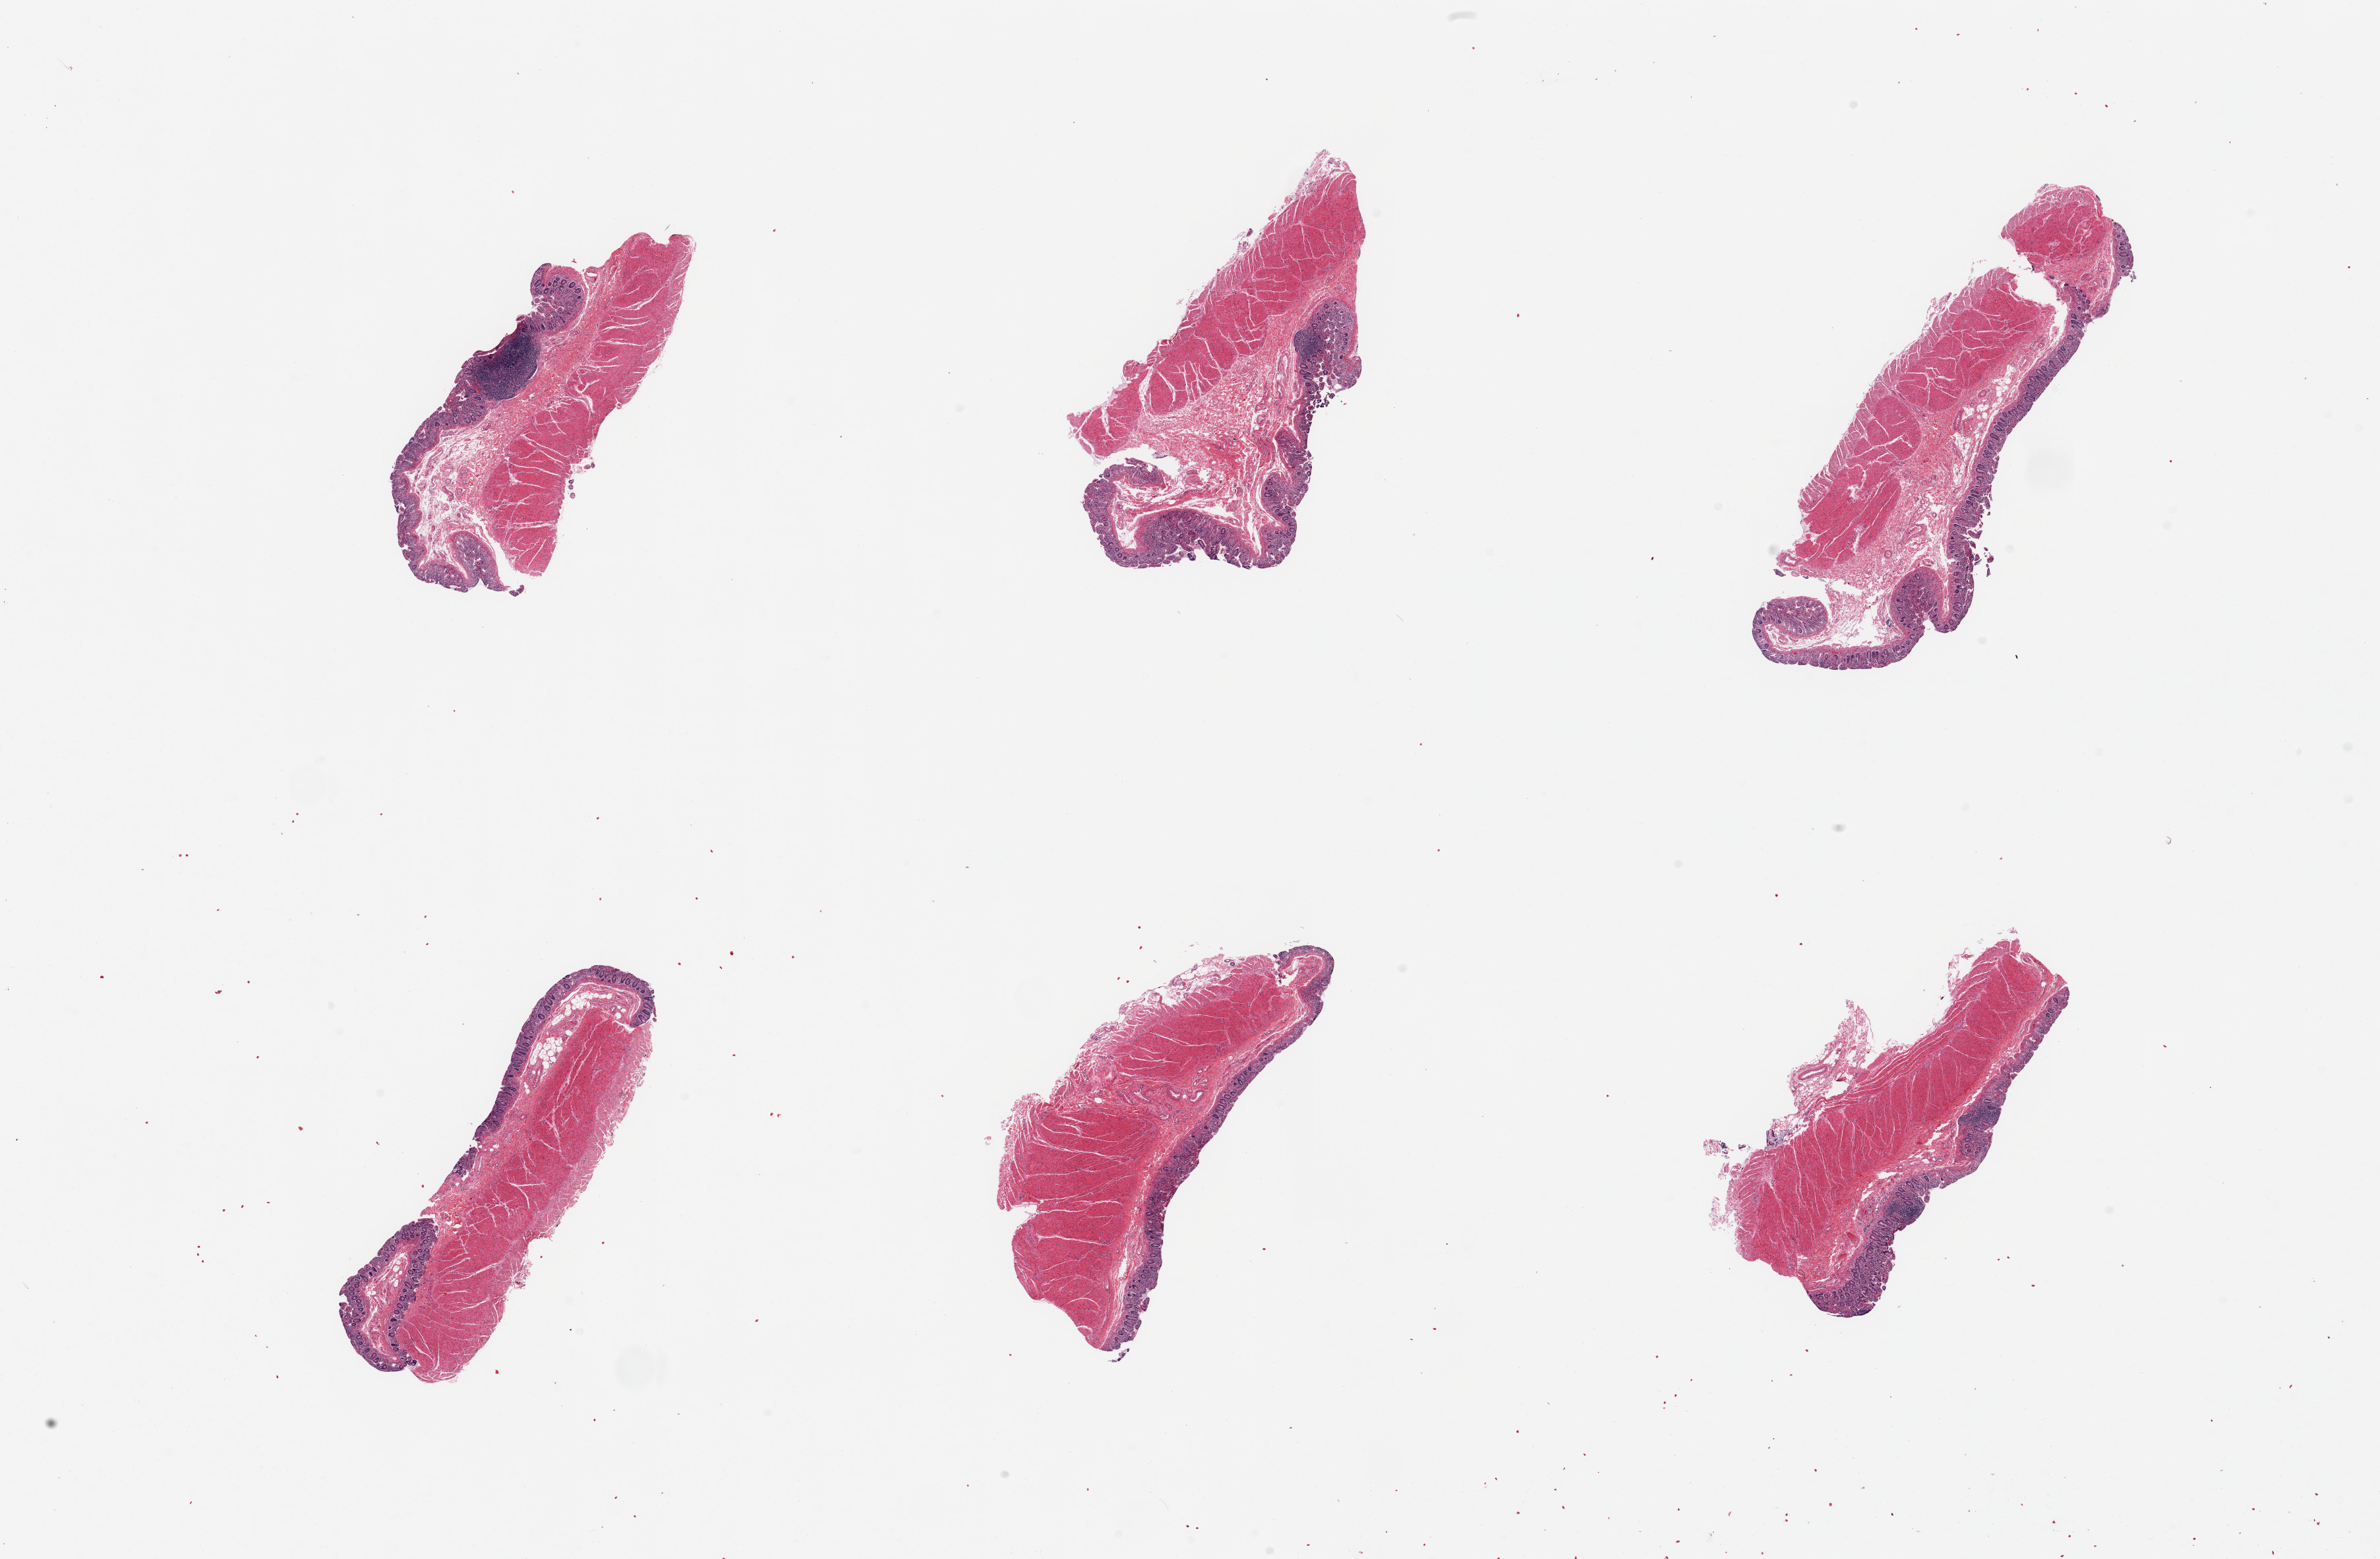
Whole-slide image, hematoxylin and eosin (H&E) stain, brightfield, low-resolution overview of the scanned area, about 28.5 x 18.7 mm; PAXgene-fixed paraffin-embedded (PFPE) section; section of ileum (target tissue); tissue donor sample. Donor: male.
* review note (as recorded): 6 pieces; full thickness sections (muscularis not target) with partially autolyzed mucosa, rare lymphoid aggregate